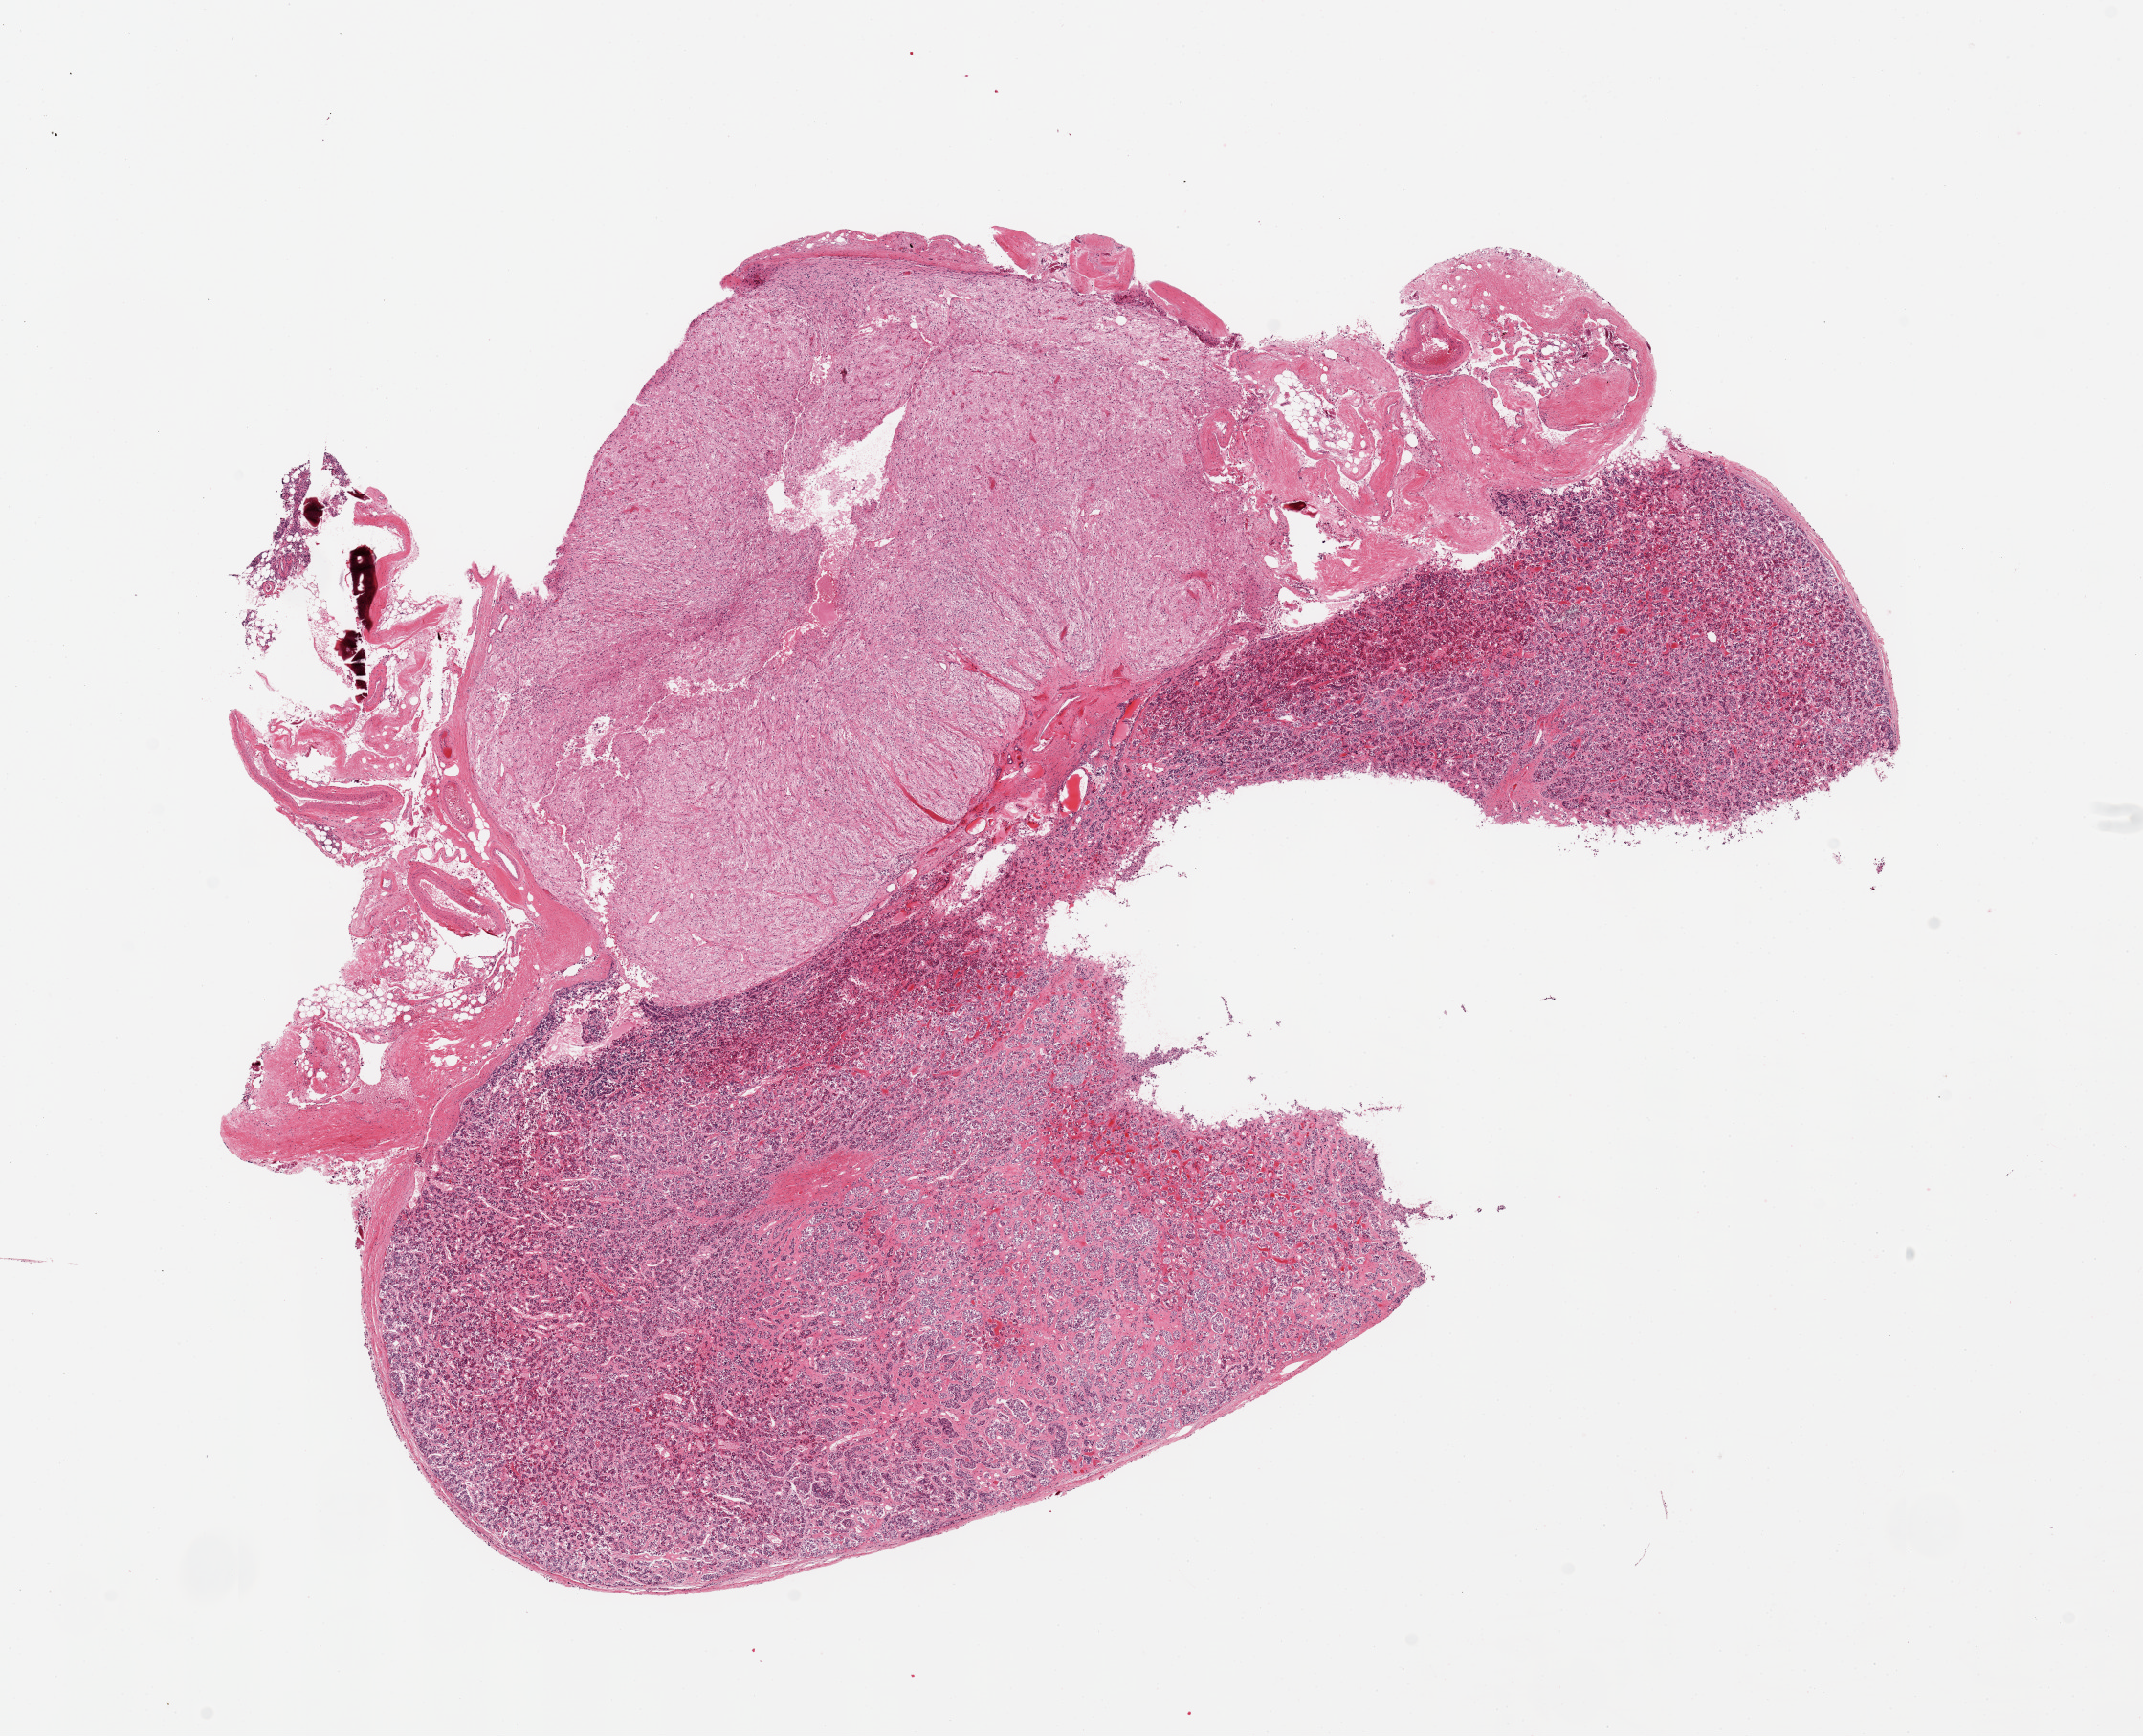
H&E whole-slide image — whole scanned area (about 17.7 x 14.4 mm, slide scanned at 20x) shown as a low-resolution overview. PAXgene-fixed paraffin-embedded (PFPE) section. Sampled site (target tissue): pituitary. Donor tissue sample. Donor sex: male.
Pathologist's review note for this sample: 1 piece, ~40% neurohypophysis, ~7mm piece, 13x5mm adenohypophysis, rest is adherent dura.